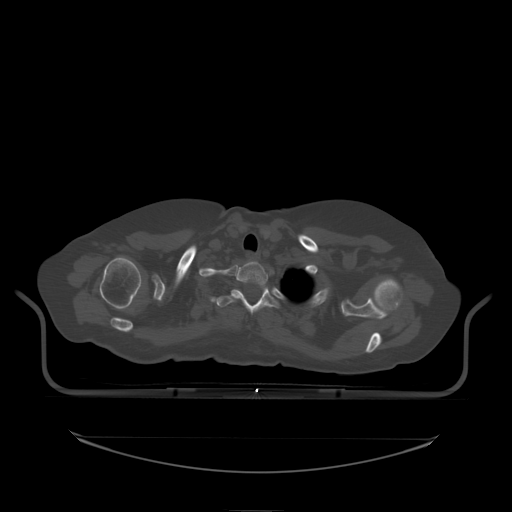
CT including the spine, one axial slice; position 183 of 242 along the scan axis; bone window (W 1800 / L 400 HU); 512 × 512 image matrix. Female patient, age 53 years. From the clinical record (not read from this slice): primary cancer: lung.
Outlined on this slice (semi-automatically segmented with operator editing):
- T1 vertebra: bounding box <236,261,269,289> (left, top, right, bottom; pixels)
- T2 vertebra: <217,287,280,314>